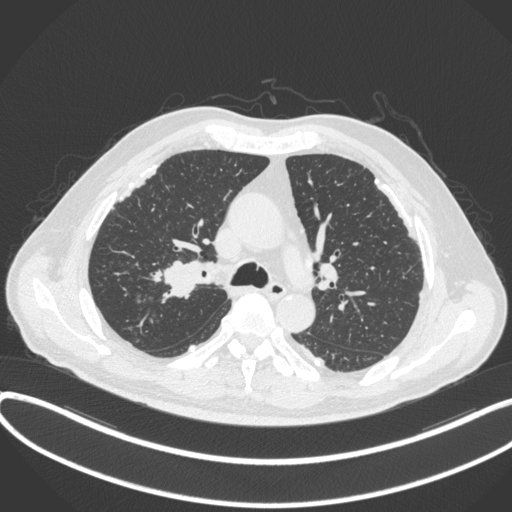
Chest CT, one axial slice; slice 283 of 455 in the series (ordered by position); reconstruction kernel B31f; 120 kVp; lung window (W 1500 / L -600 HU); 1 mm slice thickness; 512 × 512 image matrix, field of view 400 × 400 mm. Patient: male, 58 years. Case-level facts recorded for this patient, not image findings: clinical TNM (as recorded): T1c N0 M0.
Structures marked on this image (bounding box drawn by a radiologist):
- lung tumour (recorded histology: squamous cell carcinoma): bounding box [x1, y1, x2, y2] px = [152, 252, 209, 306]